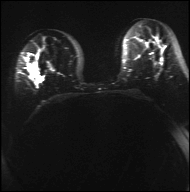
Breast MRI, one axial slice. Diffusion-weighted series; image 2 of 4 stored at this slice position (different b-values; order by instance number). 3 T. 4 mm slice thickness. 190 × 192 image matrix, field of view 317 × 320 mm. Female patient.
Outlined on this slice (manually delineated by an expert):
- tumour on diffusion-weighted imaging: bounding box [x1, y1, x2, y2] px = [77, 64, 97, 75]